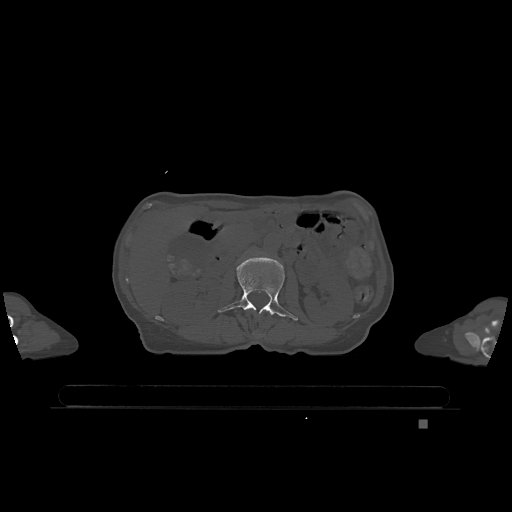
CT including the spine, one axial slice. Slice 418 of 1317 in the series (ordered by position). Bone window (W 1800 / L 400 HU). 0.5 mm slice thickness. 512 × 512 image matrix. Patient: female, 74 years. From the clinical record (not read from this slice): primary cancer: lung.
Annotated regions visible in this slice (semi-automatically segmented with operator editing):
- L2 vertebra: bounding box (x1, y1, x2, y2) in pixels: (218, 257, 298, 321)